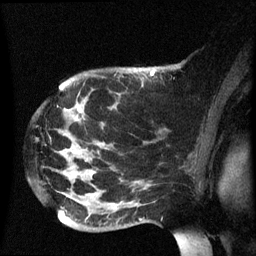
Breast MRI (dynamic contrast-enhanced), one sagittal slice; slice 44 of 60 in the series (ordered by position); dynamic contrast-enhanced series, image 2 of 3 at this slice position (ordered by acquisition); 1.5 T; TE 4.2 ms, TR 8.4 ms; 256 × 256 image matrix, field of view 220 × 220 mm. Female patient, age 49 years.
Annotated regions visible in this slice (semi-automatically segmented with operator editing):
- analysis volume of interest (the breast-tissue region the enhancement analysis was run in; not a lesion): bounding box [x1, y1, x2, y2] px = [42, 72, 185, 235]
- tumour enhancement mask (voxels above the 70 % enhancement threshold inside the analysis volume of interest): [152, 72, 155, 75]